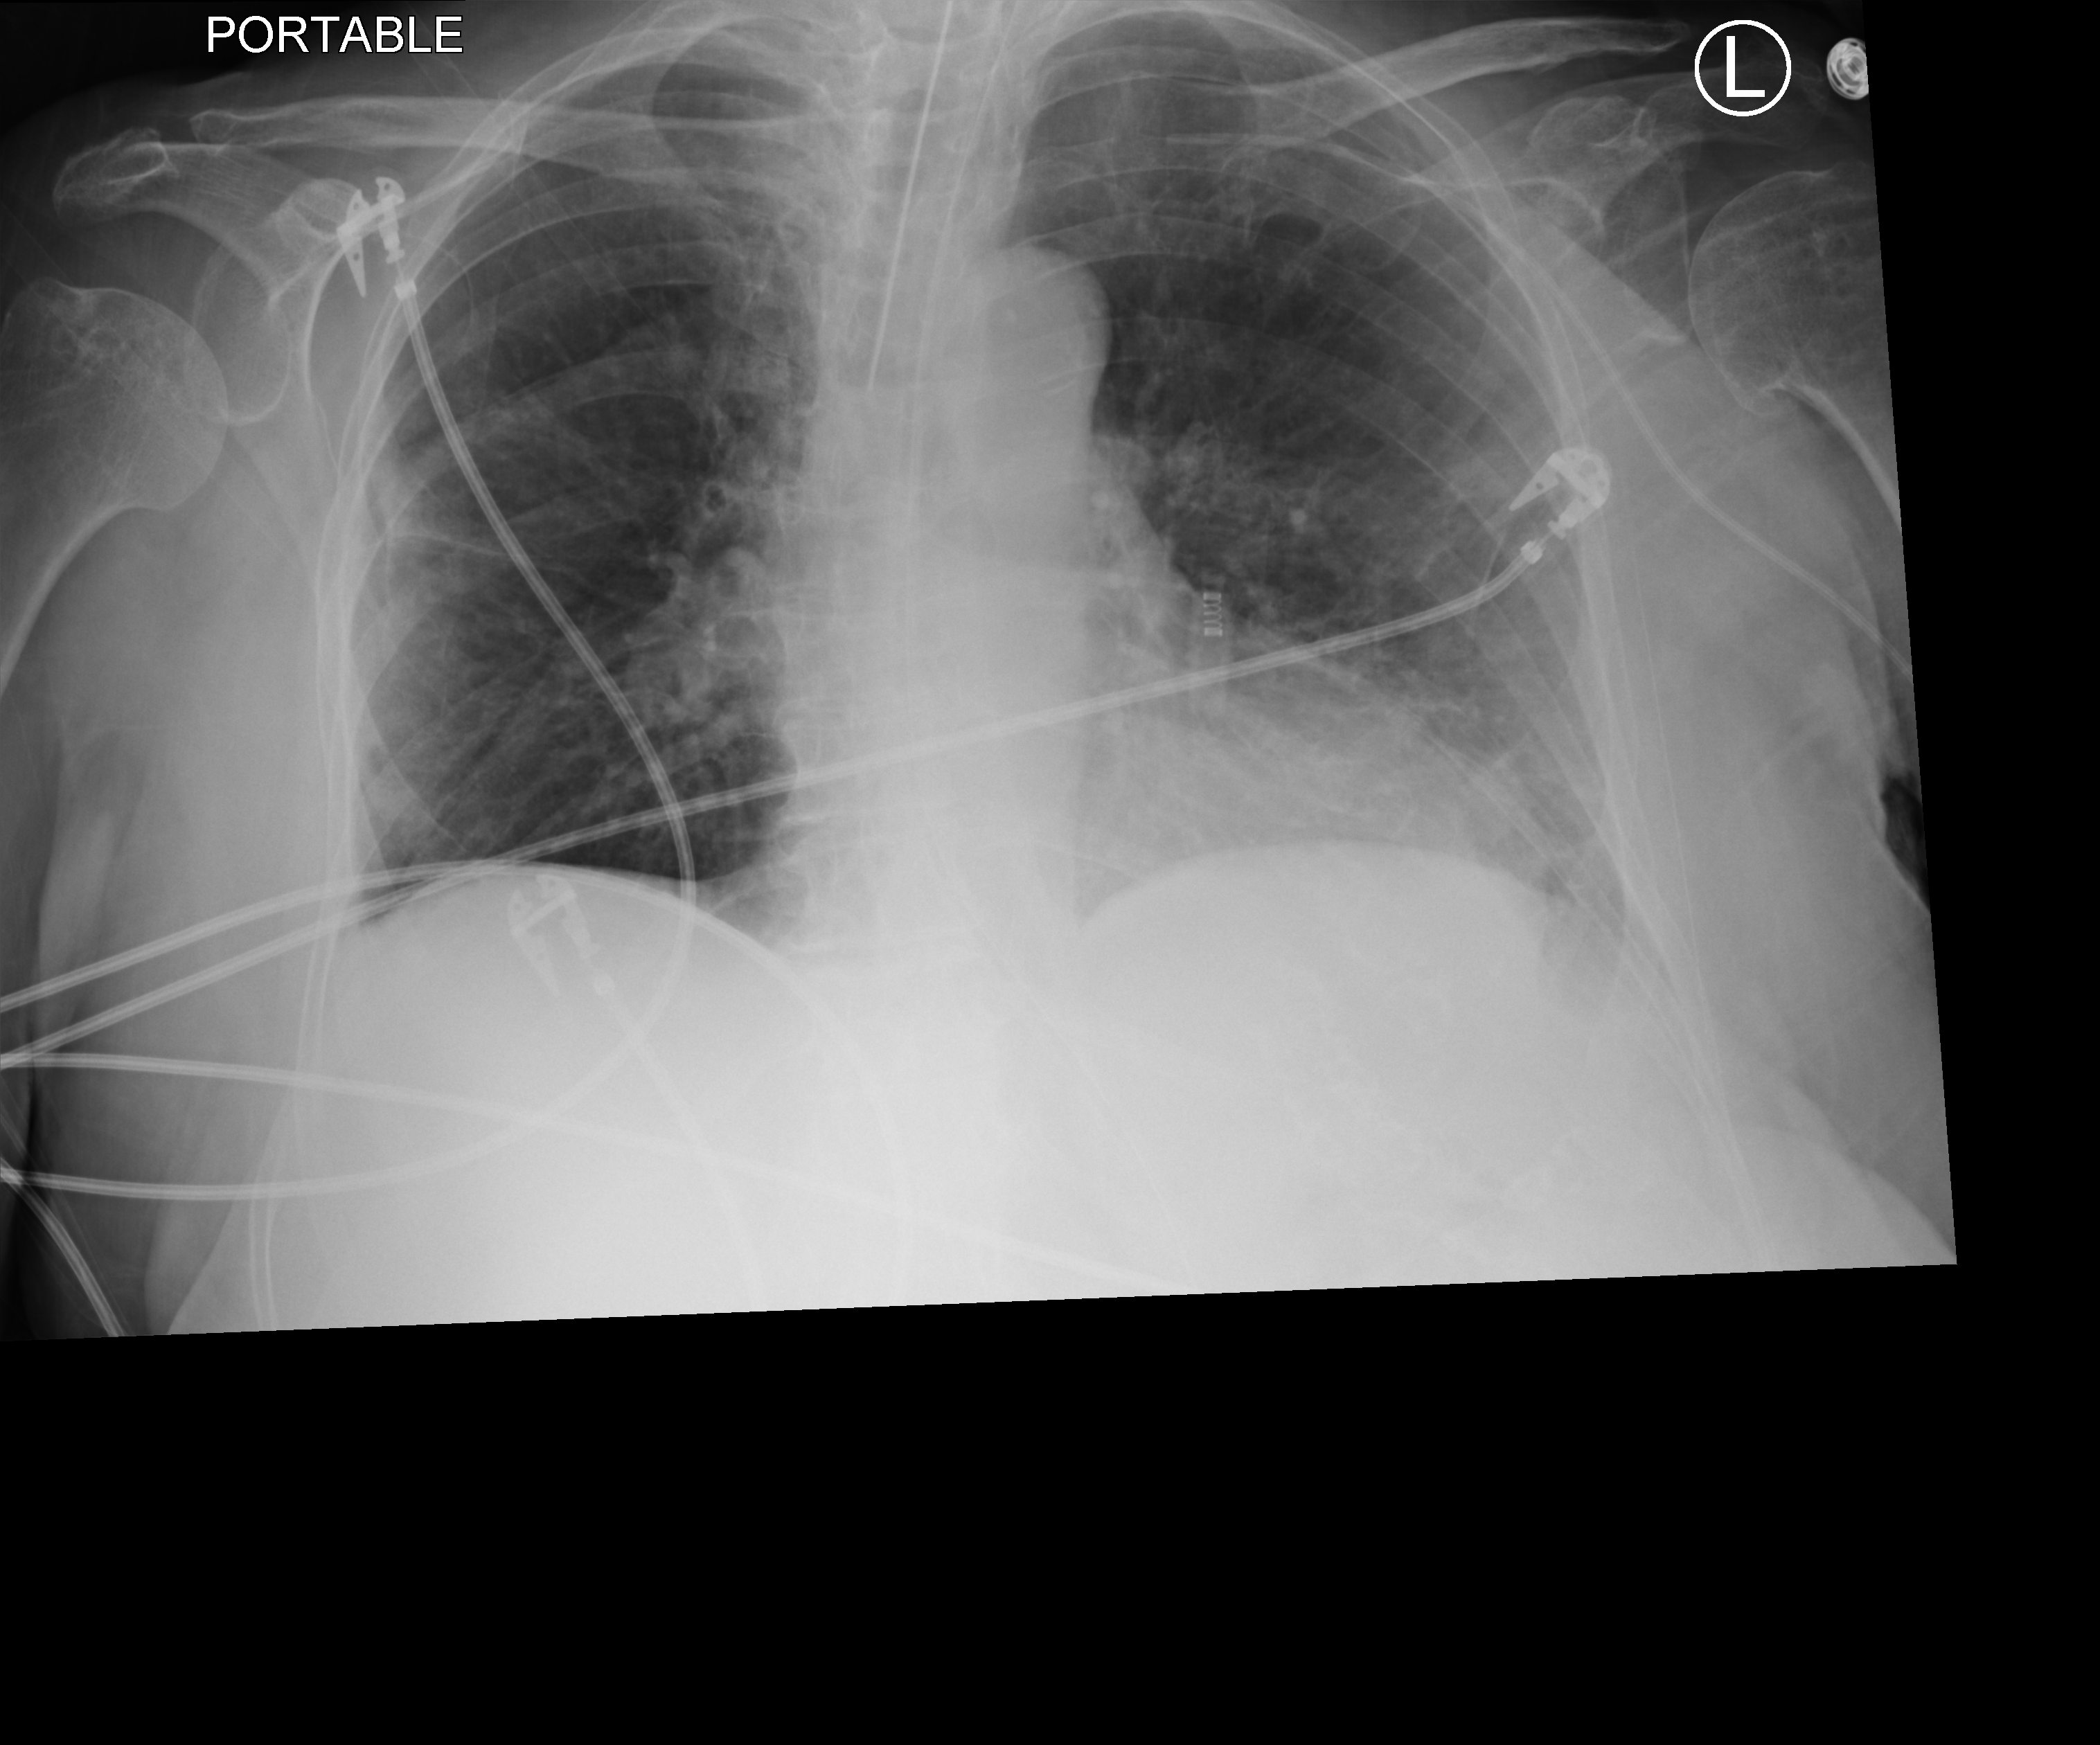
Portable chest radiograph, anteroposterior (AP) projection. Female patient hospitalised with COVID-19, age 75–90 years.
Admission-level facts for this patient (not findings on this image; timing relative to this image not recorded): mechanically ventilated during this hospital stay: yes; admitted to intensive care during this hospital stay: yes; COPD (admission record): no.